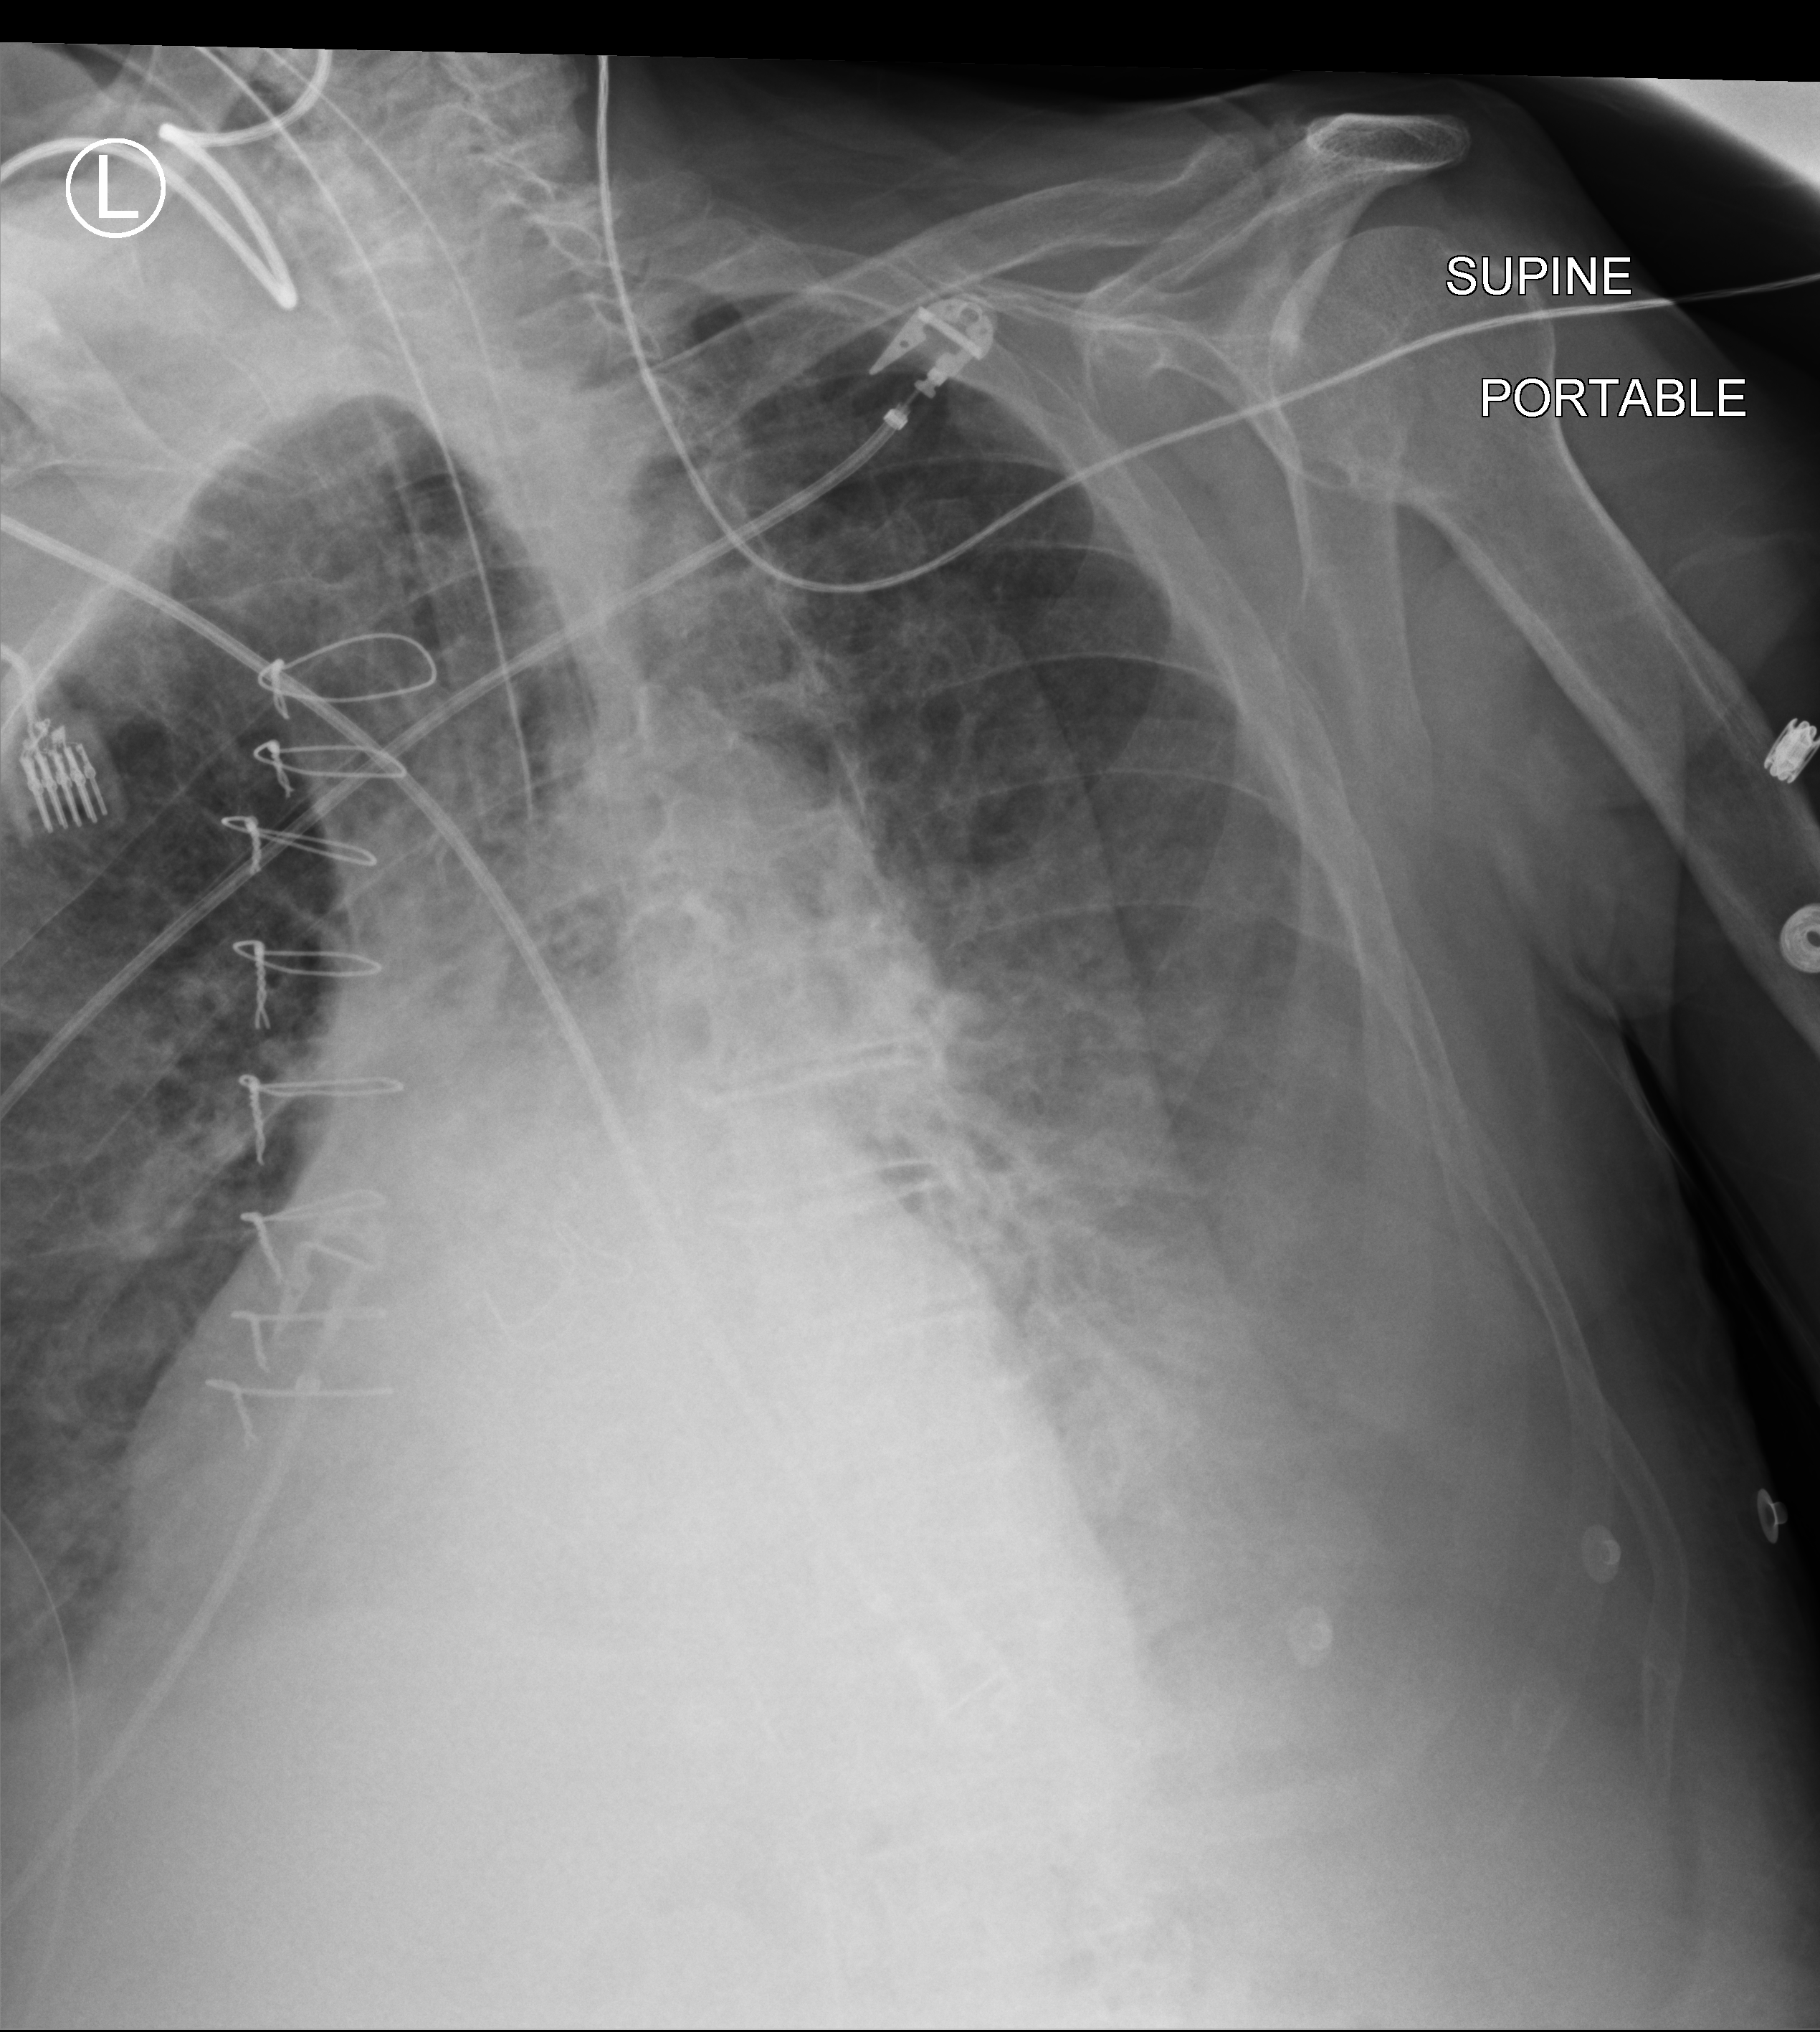
Portable chest radiograph, anteroposterior (AP) projection. Male patient hospitalised with COVID-19, age 75–90 years.
Admission-level facts for this patient (not findings on this image; timing relative to this image not recorded): length of hospital stay: 40 days; admitted to intensive care during this hospital stay: yes; mechanically ventilated during this hospital stay: yes.